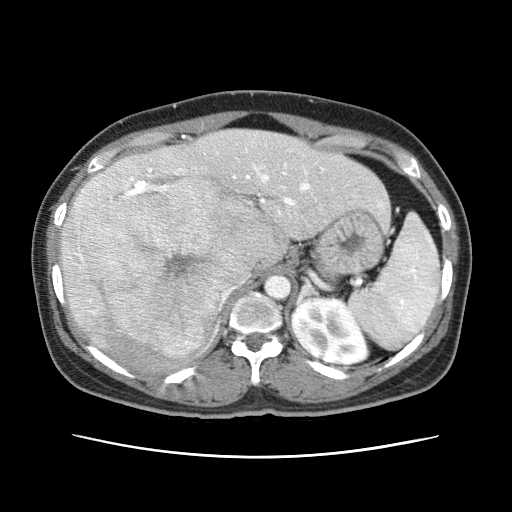
Contrast-enhanced abdominal CT (liver protocol), one axial slice. Position 42 of 79 along the scan axis. Reconstruction kernel STANDARD. 120 kVp. Soft-tissue window (W 400 / L 40 HU). 2.5 mm slice thickness. 512 × 512 image matrix, field of view 340 × 340 mm. Case-level facts recorded for this patient, not image findings: diagnosis: hepatocellular carcinoma (patient treated with transarterial chemoembolisation; whether this scan precedes or follows treatment is not stated here); TNM stage (as recorded): Stage-I; Child-Pugh class: A.
Annotated regions visible in this slice (semi-automatic segmentation, software-assisted and operator-edited):
- abdominal aorta: bounding box <265,273,292,299> (left, top, right, bottom; pixels)
- liver parenchyma outside the tumour (the mass and vessels are separate outlines, so this box may not span the whole liver): <60,130,389,364>
- mass: <69,173,288,357>
- liver vessels: <77,167,380,300>